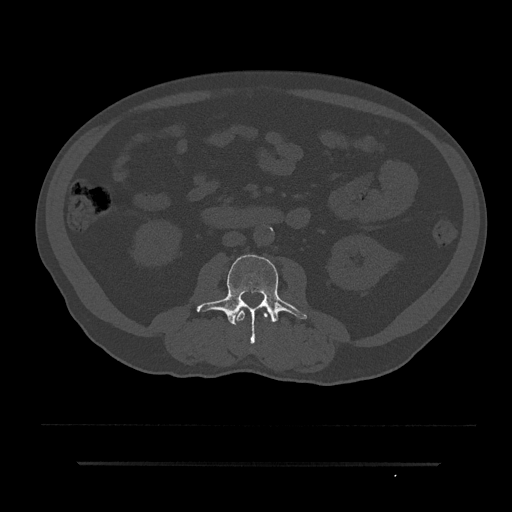
CT including the spine, one axial slice. Slice 16 of 797 in the series (ordered by position). Bone window (W 1800 / L 400 HU). 512 × 512 image matrix, field of view 464 × 464 mm. Male patient, age 59 years. From the clinical record (not read from this slice): primary cancer: bile ducts; vertebrae with lytic lesions (as recorded): T10.
Annotated regions visible in this slice (semi-automatic segmentation, software-assisted and operator-edited):
- L2 vertebra: box from (x=234, y=308) to (x=272, y=322) px
- L3 vertebra: (x=196, y=255)–(x=307, y=344)